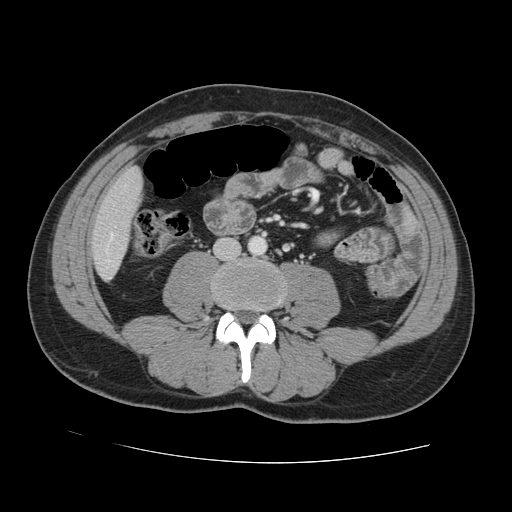
Contrast-enhanced abdominal CT, one axial slice. Slice 21 of 131 in the series (ordered by position). 120 kVp. Intravenous contrast given. Soft-tissue window (W 400 / L 40 HU). 512 × 512 image matrix, field of view 380 × 380 mm. Male patient, age 40 years. Case-level facts recorded for this patient, not image findings: diagnosis: colorectal cancer liver metastases, imaged before liver resection; multiple liver metastases: yes.
Outlined on this slice (outlined manually by an expert reader):
- hepatic veins: bounding box [x1, y1, x2, y2] px = [110, 234, 113, 239]
- liver: [93, 169, 141, 278]